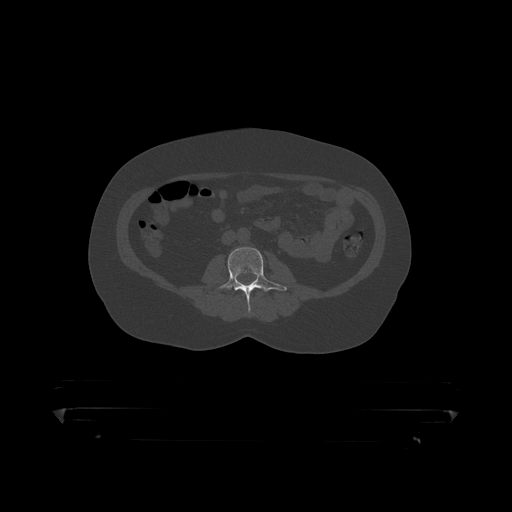
CT including the spine, one axial slice; slice 91 of 390 in the series (ordered by position); 120 kVp; bone window (W 1800 / L 400 HU); 1.25 mm slice thickness; 512 × 512 image matrix, field of view 650 × 650 mm. Patient: male, 60 years. From the clinical record (not read from this slice): primary cancer: prostate.
Annotated regions visible in this slice (semi-automatically segmented with operator editing):
- L2 vertebra: bounding box <248,292,262,314> (left, top, right, bottom; pixels)
- L3 vertebra: <216,248,287,308>